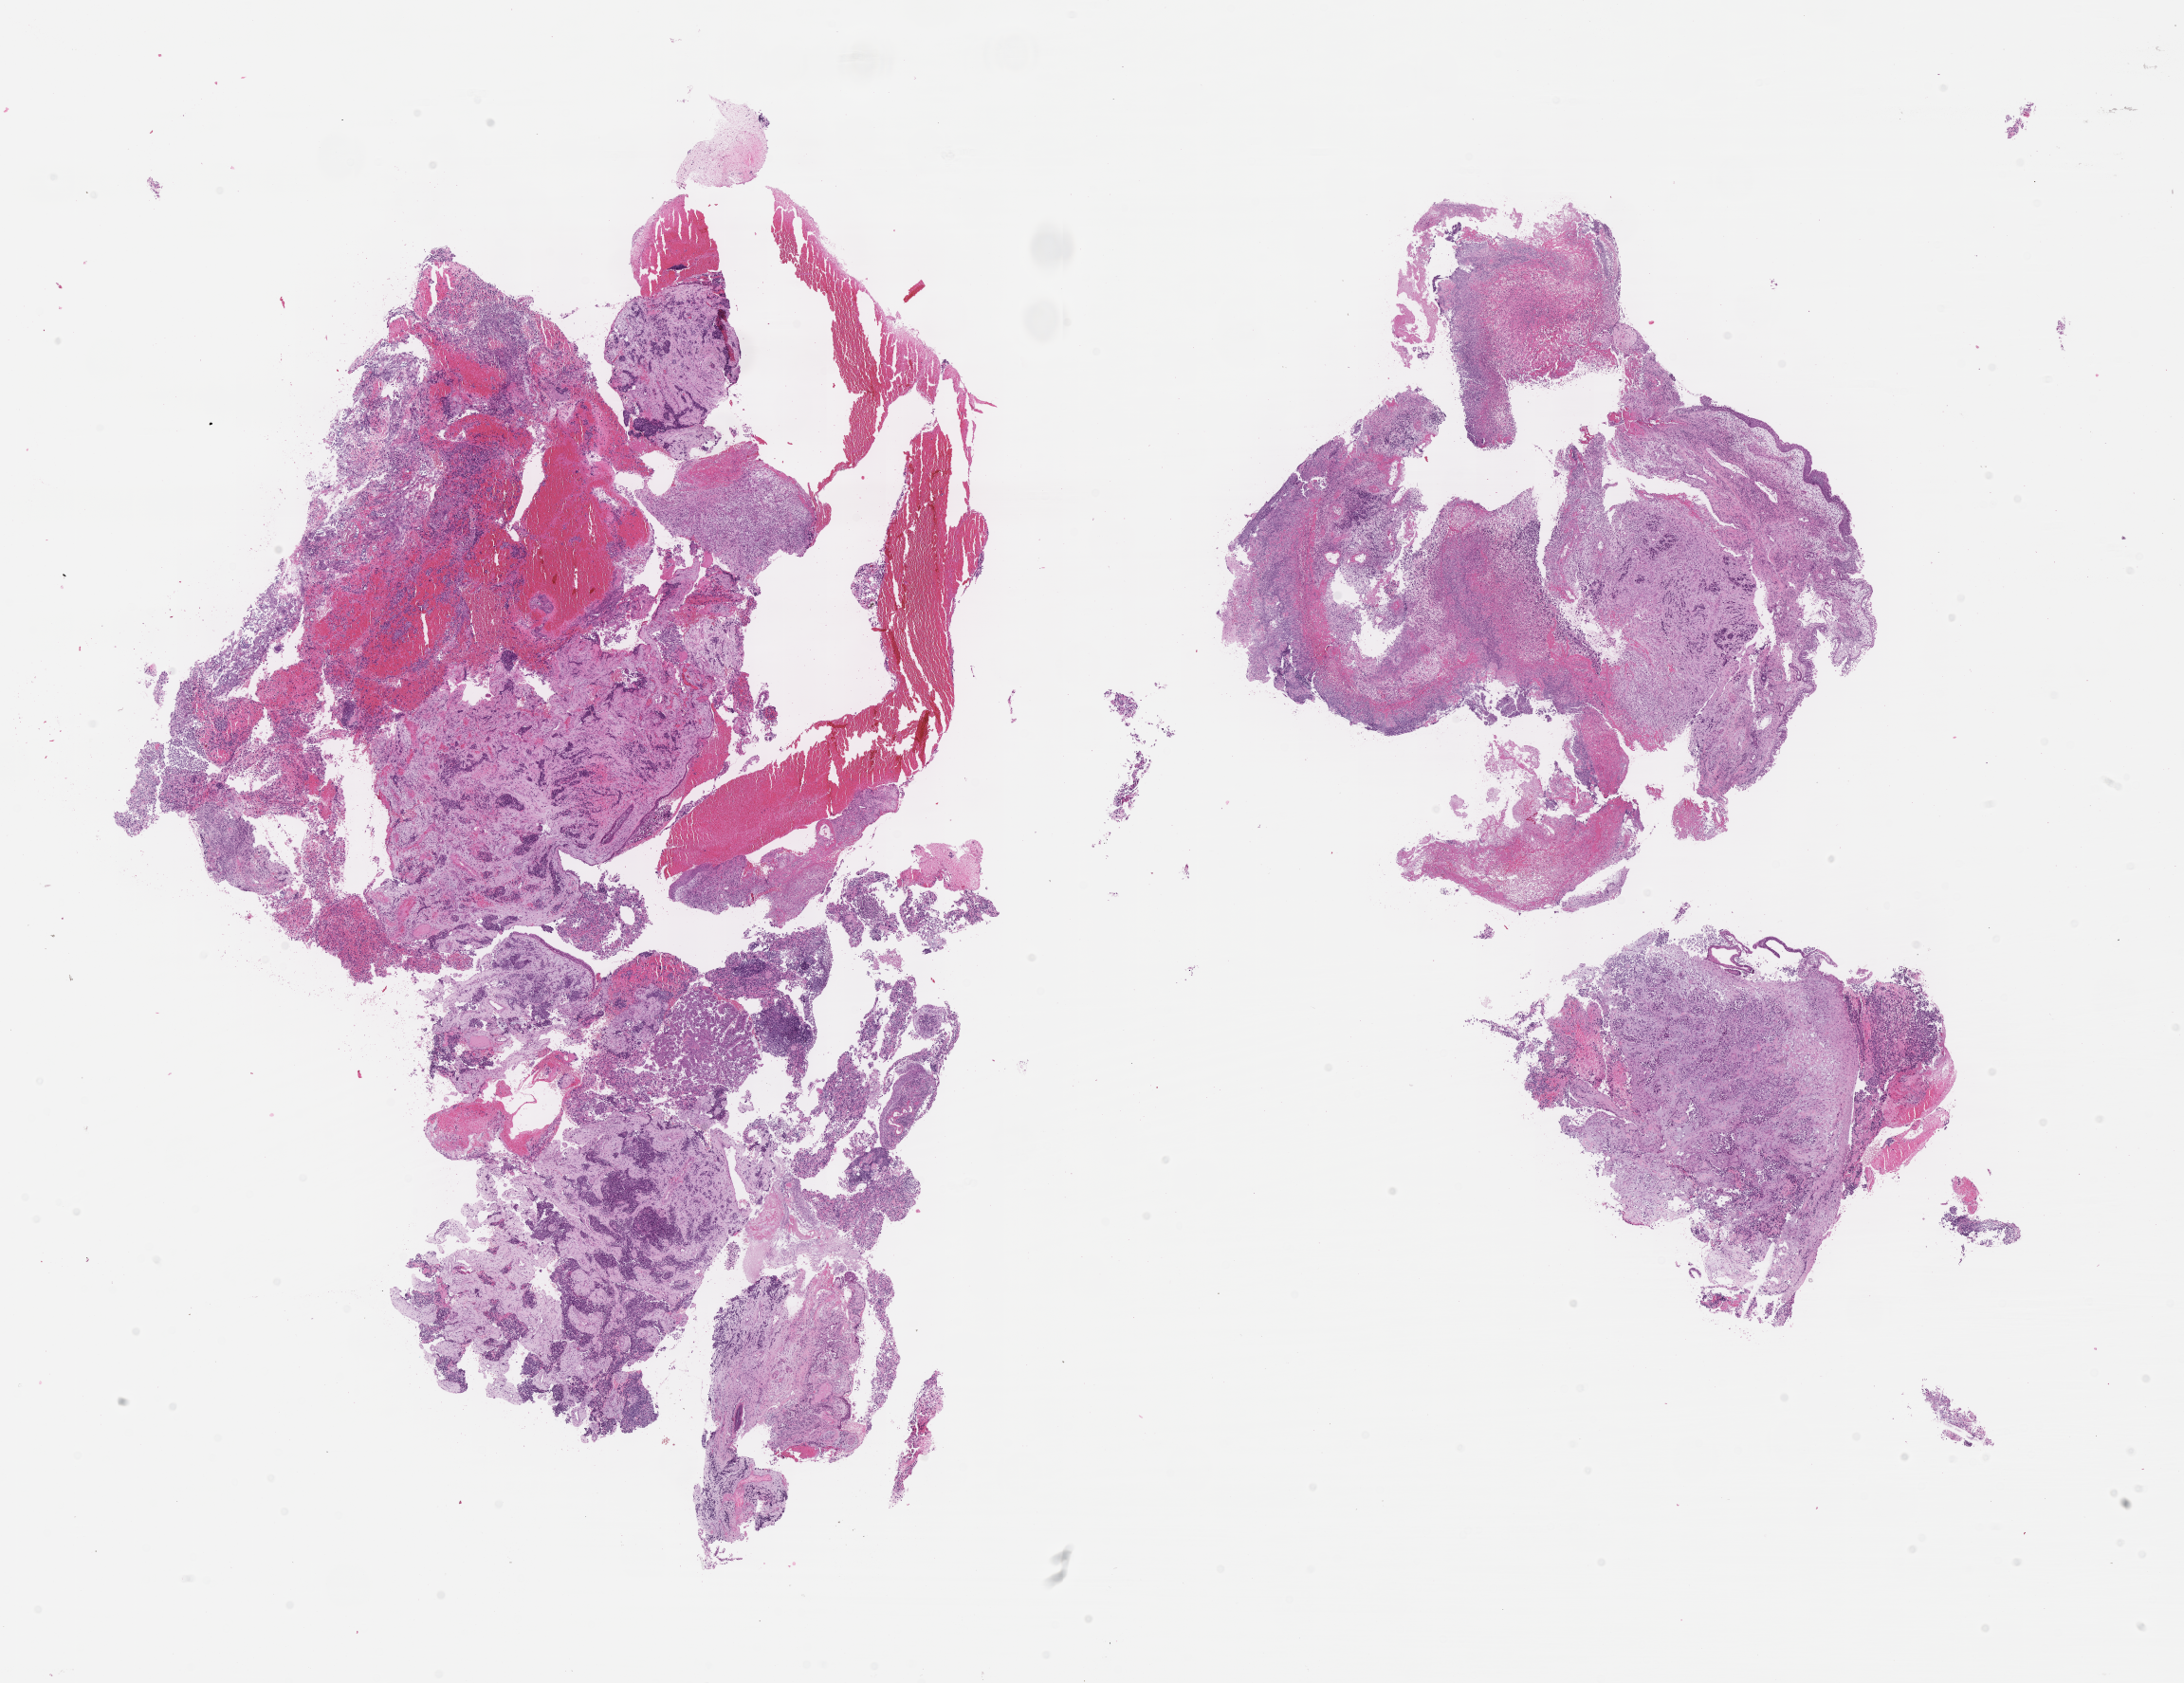
Digitized H&E-stained section of tumor tissue, shown as a low-resolution overview of the whole scanned area (about 18.6 x 14.3 mm); formalin-fixed paraffin-embedded section; sample anatomic site: nasal cavity. Male patient, age at diagnosis 11.2 years.
Diagnosis: rhabdomyosarcoma; histological classification: alveolar rhabdomyosarcoma. Stage (as recorded): 4. Metastatic status at presentation (as recorded): metastatic (confirmed).